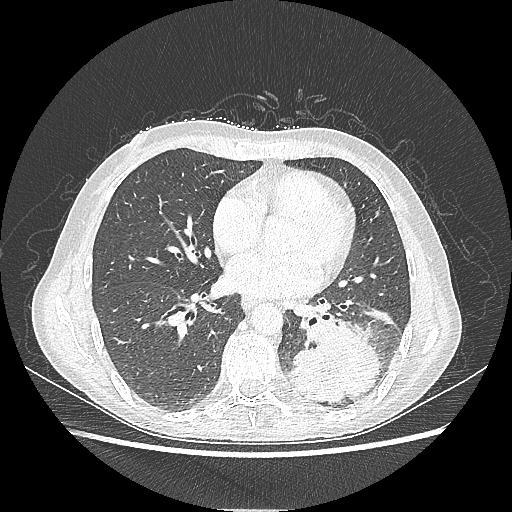
Chest CT, one axial slice. Position 98 of 220 along the scan axis. Reconstruction kernel LUNG. 80 kVp. Lung window (W 1500 / L -600 HU). 1.25 mm slice thickness. 512 × 512 image matrix, field of view 360 × 360 mm. Female patient, age 53 years. From the clinical record (not read from this slice): clinical TNM (as recorded): T3 N0 M0.
Structures marked on this image (bounding box drawn by a radiologist):
- lung tumour (recorded histology: adenocarcinoma): bounding box <285,311,382,403> (left, top, right, bottom; pixels)